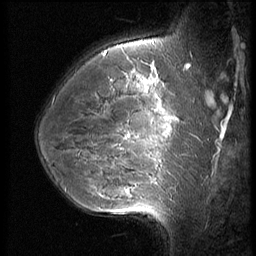
Breast MRI (dynamic contrast-enhanced), one sagittal slice. Position 42 of 56 along the scan axis. 3 images stored at this slice position (order not interpretable as contrast timing). 1.5 T. TE 4.2 ms, TR 9 ms. 256 × 256 image matrix, field of view 180 × 180 mm. Female patient, age 35 years. From the clinical record (not read from this slice): setting: breast cancer imaged before/during neoadjuvant chemotherapy; receptor status: HR-positive, HER2-negative.
Outlined on this slice (semi-automatically segmented with operator editing):
- analysis volume of interest (the breast-tissue region the enhancement analysis was run in; not a lesion): bounding box <63,60,190,218> (left, top, right, bottom; pixels)
- tumour enhancement mask (voxels above the 140 % enhancement threshold inside the analysis volume of interest): <126,93,174,192>